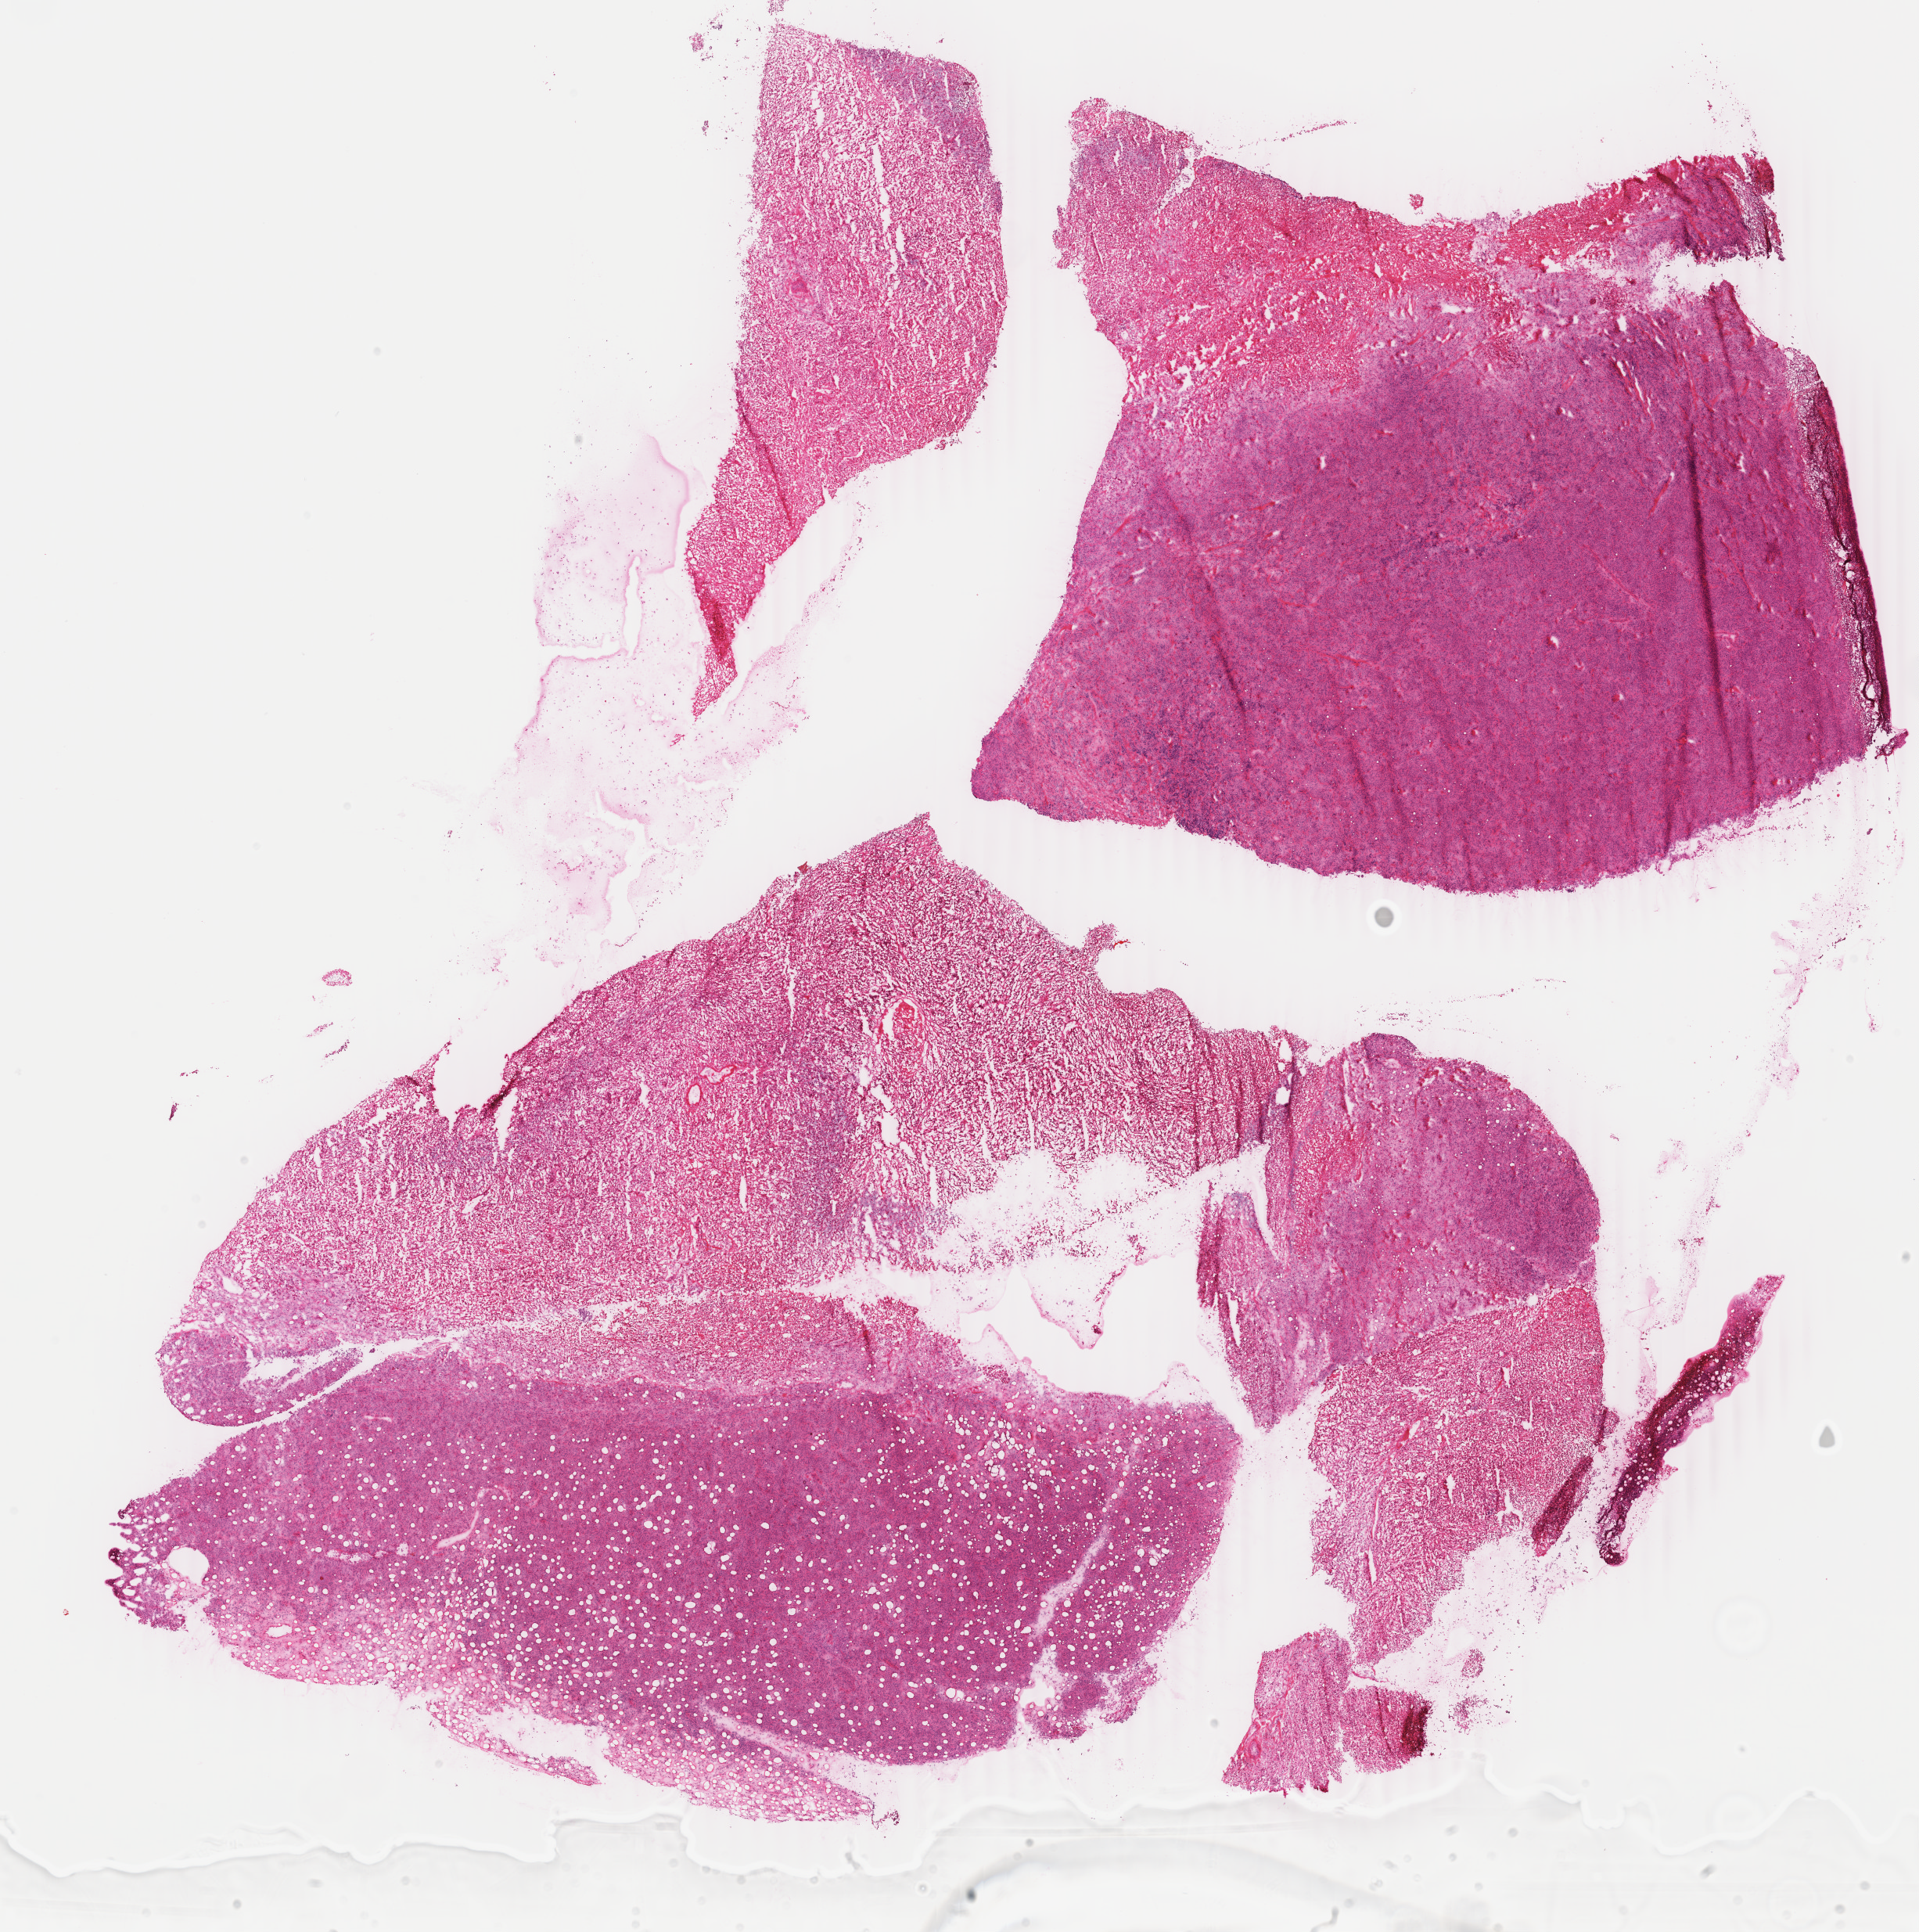
Digitized H&E tissue section (whole slide), low-resolution overview of the scanned area, about 19.5 x 19.6 mm. Frozen section from the top of the tissue portion. Primary tumour sample from the lymphoid tissue. Female, age 57 years at initial diagnosis. Composition of this section per pathologist review: tumour cells 85%, tumour nuclei 90%, normal cells 5%, stromal cells 5%, necrosis 5%. Infiltration values recorded for this section: lymphocyte infiltration 5%, monocyte infiltration 2%, neutrophil infiltration 0%.
* pathologic diagnosis: Diffuse large B-cell lymphoma, NOS (connective, subcutaneous and other soft tissues, NOS)